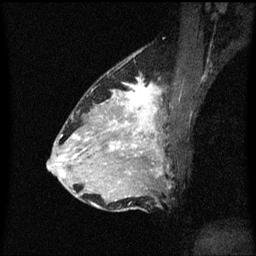
Breast MRI (dynamic contrast-enhanced), one sagittal slice. Dynamic contrast-enhanced series, image 2 of 3 at this slice position (ordered by acquisition). 1.5 T. TE 4.2 ms, TR 8.4 ms. 256 × 256 image matrix, field of view 200 × 200 mm. Female patient, age 34 years. Case-level facts recorded for this patient, not image findings: setting: breast cancer imaged before/during neoadjuvant chemotherapy; receptor status: HR-positive, HER2-negative.
Structures marked on this image (semi-automatically segmented with operator editing):
- analysis volume of interest (the breast-tissue region the enhancement analysis was run in; not a lesion): bounding box <69,70,172,209> (left, top, right, bottom; pixels)
- tumour enhancement mask (voxels above the 70 % enhancement threshold inside the analysis volume of interest): <109,80,162,175>